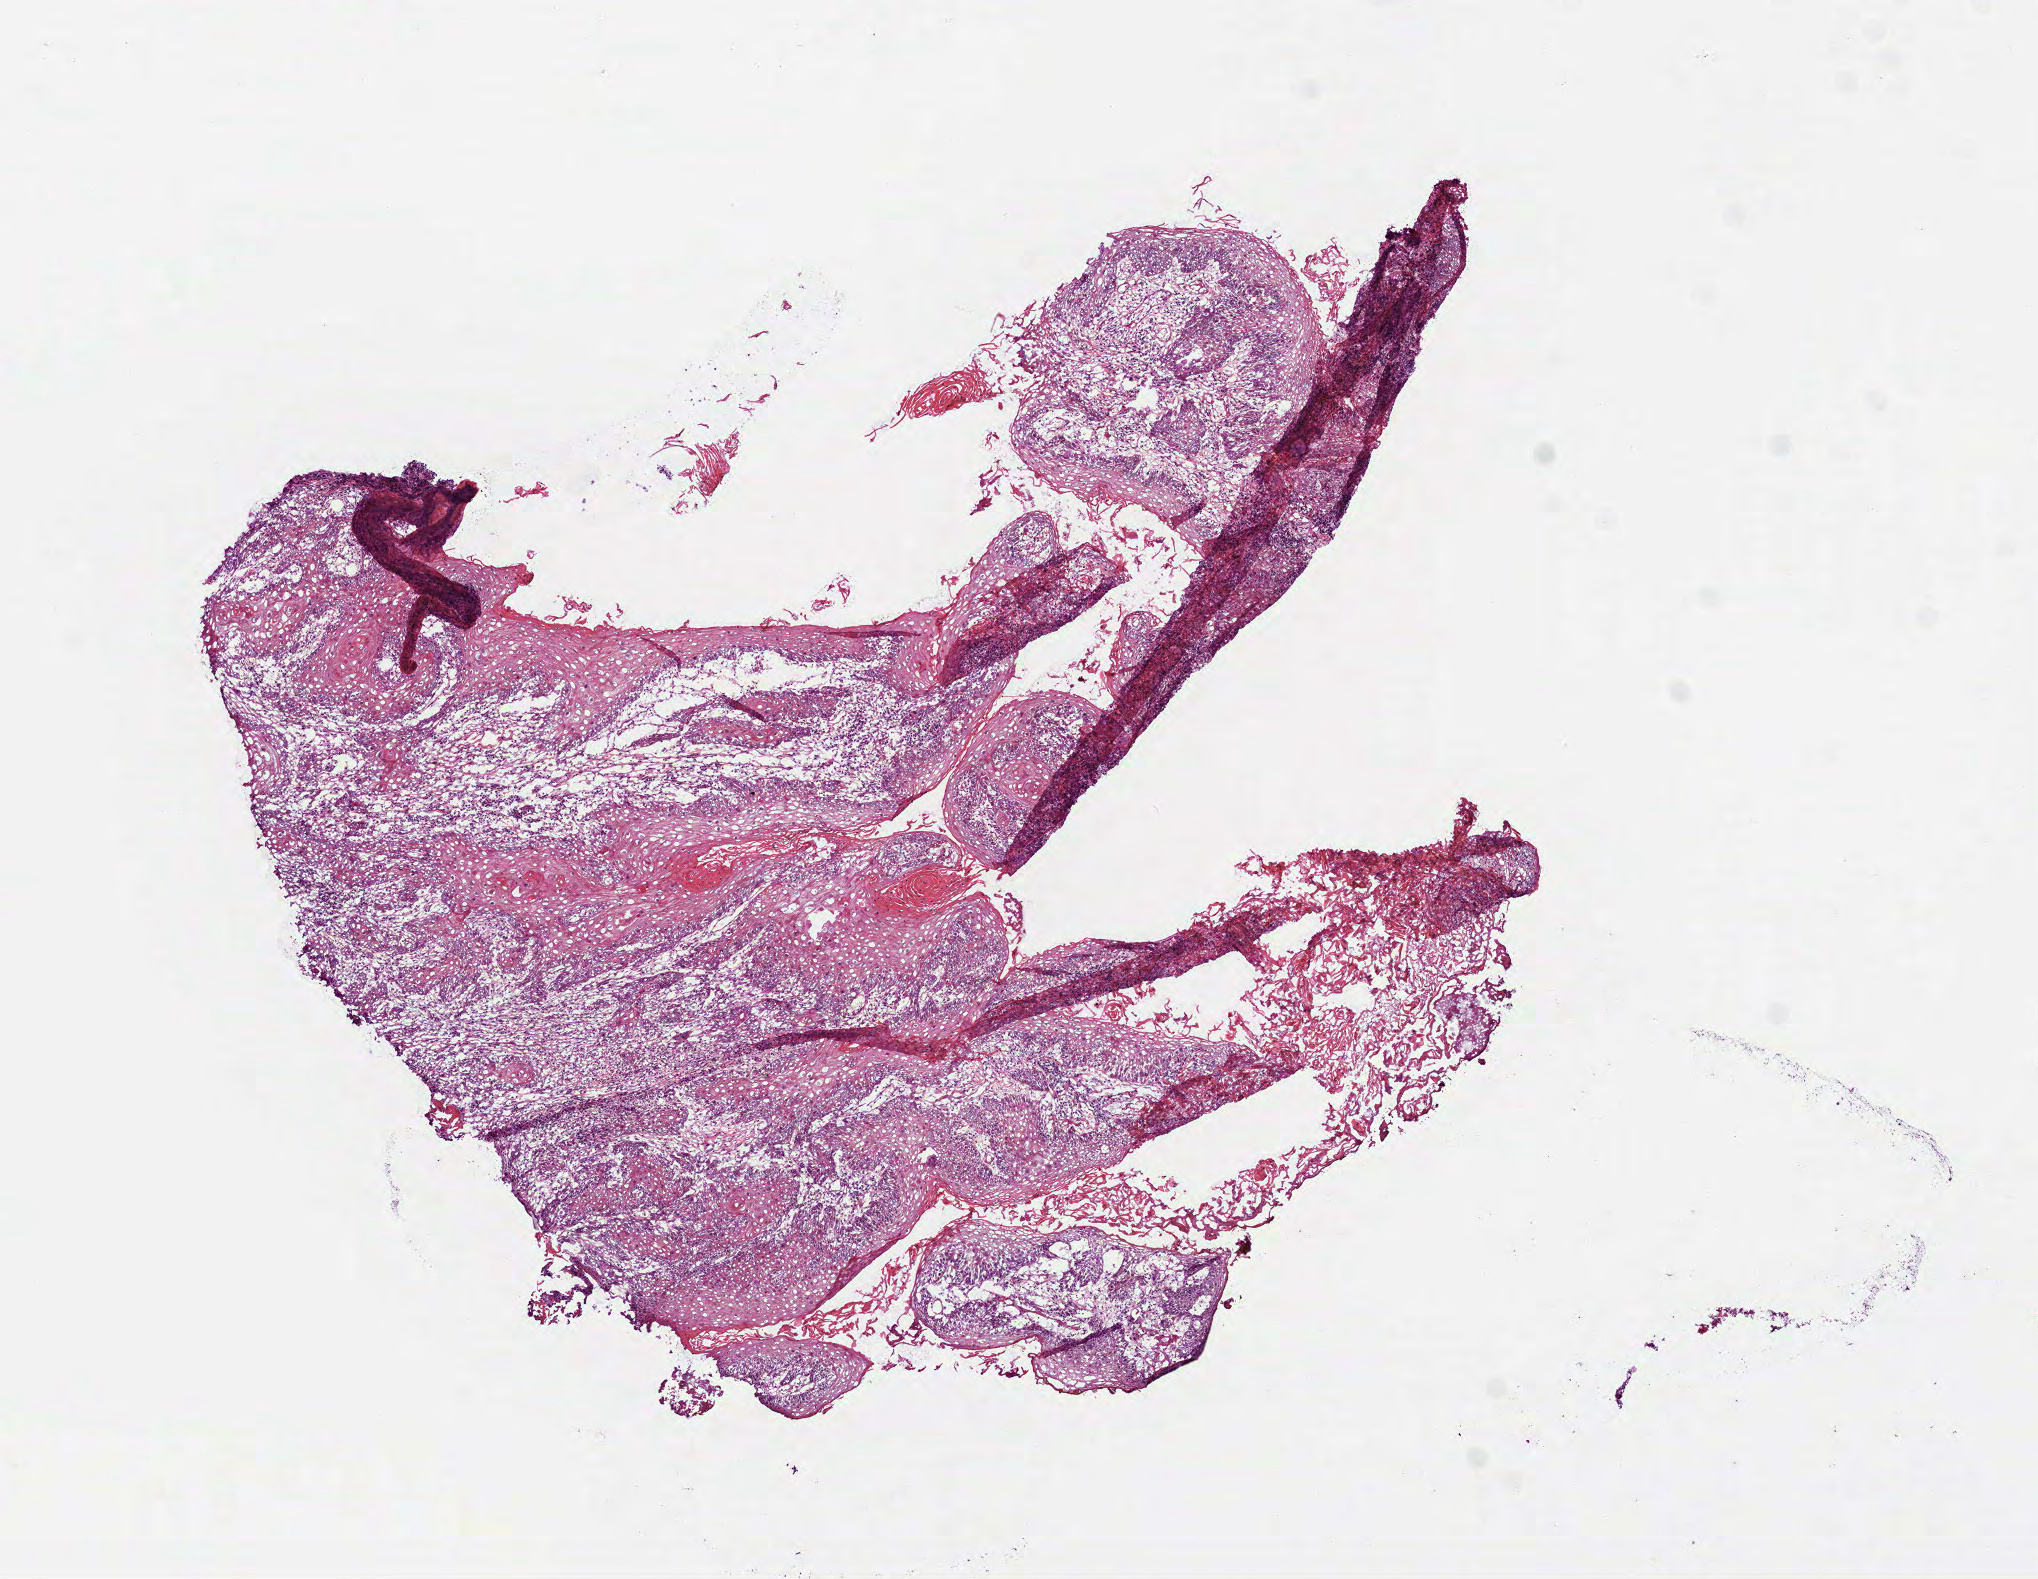
Digitized Hematoxylin and eosin (H&E) stained tissue section (whole slide) — low-resolution overview of the scanned area, about 8.2 x 6.4 mm; frozen section; head and neck, primary tumour sample. Female patient; age at initial diagnosis 76 years. Histologic grade: G2 (moderately differentiated). Pathologist review of this section (percent, as recorded): tumour cells 85%, tumour nuclei 60%, normal cells 0%, stromal cells 15%, necrosis 0%. Inflammatory infiltration, as recorded: lymphocyte infiltration 35%.
* pathologic diagnosis: Squamous cell carcinoma, NOS (mouth, NOS)
* AJCC pathologic stage: III (7th edition)
* laterality: left